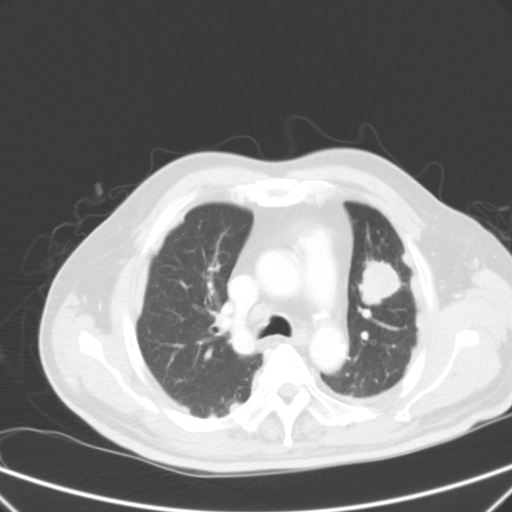
Chest CT, one axial slice; slice 41 of 59 in the series (ordered by position); 120 kVp; intravenous contrast given; lung window (W 1500 / L -600 HU); 5 mm slice thickness; 512 × 512 image matrix. Male patient, age 66 years. From the clinical record (not read from this slice): clinical TNM (as recorded): T1c N3 M1a.
Annotated regions visible in this slice (rectangle marked by the reading radiologist):
- lung tumour (recorded histology: squamous cell carcinoma): bounding box <354,246,409,307> (left, top, right, bottom; pixels)